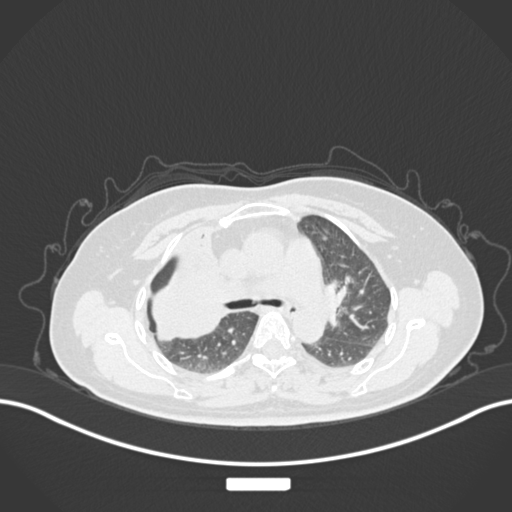
Chest CT, one axial slice. Slice 100 of 177 in the series (ordered by position). 120 kVp. Lung window (W 1500 / L -600 HU). 1 mm slice thickness. 512 × 512 image matrix, field of view 400 × 400 mm. Female patient, age 60 years. Case-level facts recorded for this patient, not image findings: clinical TNM (as recorded): T3 N1 M1.
Annotated regions visible in this slice (rectangle marked by the reading radiologist):
- lung tumour (recorded histology: adenocarcinoma): bounding box (x1, y1, x2, y2) in pixels: (138, 240, 238, 353)